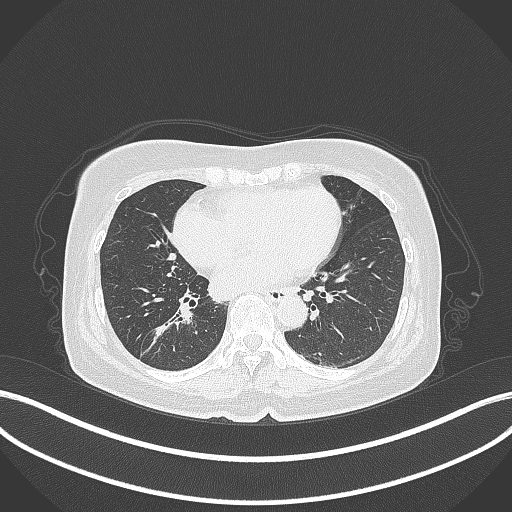
Chest CT, one axial slice; slice 166 of 429 in the series (ordered by position); reconstruction kernel B70f; lung window (W 1500 / L -600 HU); 512 × 512 image matrix, field of view 400 × 400 mm. Female patient, age 67 years. Case-level facts recorded for this patient, not image findings: clinical TNM (as recorded): T1c N1 M0.
Annotated regions visible in this slice (rectangle marked by the reading radiologist):
- lung tumour (recorded histology: adenocarcinoma): bounding box (x1, y1, x2, y2) in pixels: (140, 300, 190, 357)